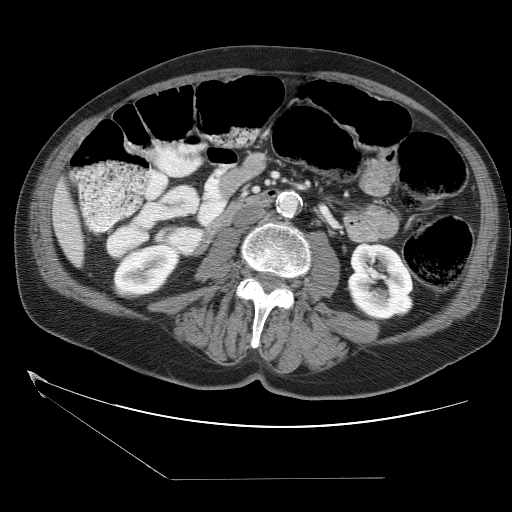
Contrast-enhanced abdominal CT (liver protocol), one axial slice. Position 2 of 38 along the scan axis. Reconstruction kernel STANDARD. 120 kVp. Soft-tissue window (W 400 / L 40 HU). 5 mm slice thickness. 512 × 512 image matrix, field of view 400 × 400 mm. Case-level facts recorded for this patient, not image findings: diagnosis: hepatocellular carcinoma (patient treated with transarterial chemoembolisation; whether this scan precedes or follows treatment is not stated here); TNM stage (as recorded): Stage-II; Child-Pugh class: A; tumour differentiation: moderately differentiated; tumour size: 0.8 cm.
Outlined on this slice (semi-automatically segmented with operator editing):
- liver parenchyma outside the tumour (the mass and vessels are separate outlines, so this box may not span the whole liver): bounding box (x1, y1, x2, y2) in pixels: (52, 181, 84, 266)